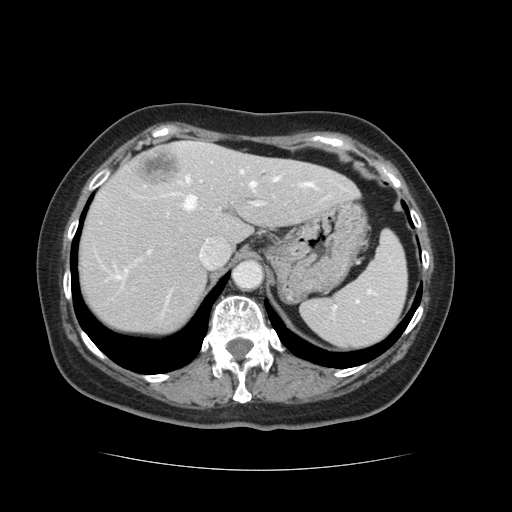
Contrast-enhanced abdominal CT, one axial slice. Position 95 of 128 along the scan axis. Intravenous contrast given. Soft-tissue window (W 400 / L 40 HU). 2.5 mm slice thickness. 512 × 512 image matrix, field of view 366 × 366 mm. Female patient, age 67 years. Case-level facts recorded for this patient, not image findings: diagnosis: colorectal cancer liver metastases, imaged before liver resection; multiple liver metastases: yes; largest metastasis: 3 cm; disease in both lobes: yes.
Outlined on this slice (expert manual segmentation):
- hepatic veins: bounding box [x1, y1, x2, y2] px = [117, 170, 314, 304]
- liver: [78, 143, 356, 335]
- planned liver remnant (the part of the liver to remain after resection): [78, 156, 356, 335]
- portal vein (with intrahepatic branches): [149, 160, 265, 253]
- liver metastasis: [136, 149, 179, 188]